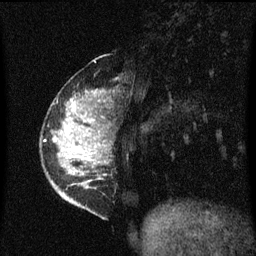
Breast MRI (dynamic contrast-enhanced), one sagittal slice; slice 18 of 60 in the series (ordered by position); dynamic contrast-enhanced series, image 2 of 3 at this slice position (ordered by acquisition); 1.5 T; TE 4.2 ms, TR 8.4 ms; 2 mm slice thickness; 256 × 256 image matrix, field of view 200 × 200 mm. Female patient, age 34 years. Case-level facts recorded for this patient, not image findings: setting: breast cancer imaged before/during neoadjuvant chemotherapy; receptor status: HR-positive, HER2-negative.
Structures marked on this image (semi-automatically segmented with operator editing):
- analysis volume of interest (the breast-tissue region the enhancement analysis was run in; not a lesion): bounding box (x1, y1, x2, y2) in pixels: (42, 58, 111, 215)
- tumour enhancement mask (voxels above the 70 % enhancement threshold inside the analysis volume of interest): (66, 104, 75, 145)